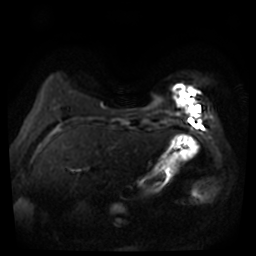
Breast MRI, one axial slice; slice 9 of 44 in the series (ordered by position); diffusion-weighted series; image 2 of 4 stored at this slice position (different b-values; order by instance number); 3 T; 256 × 256 image matrix, field of view 360 × 360 mm. Female patient.
Annotated regions visible in this slice (manually delineated by an expert):
- tumour on diffusion-weighted imaging: bounding box [x1, y1, x2, y2] px = [177, 89, 194, 107]